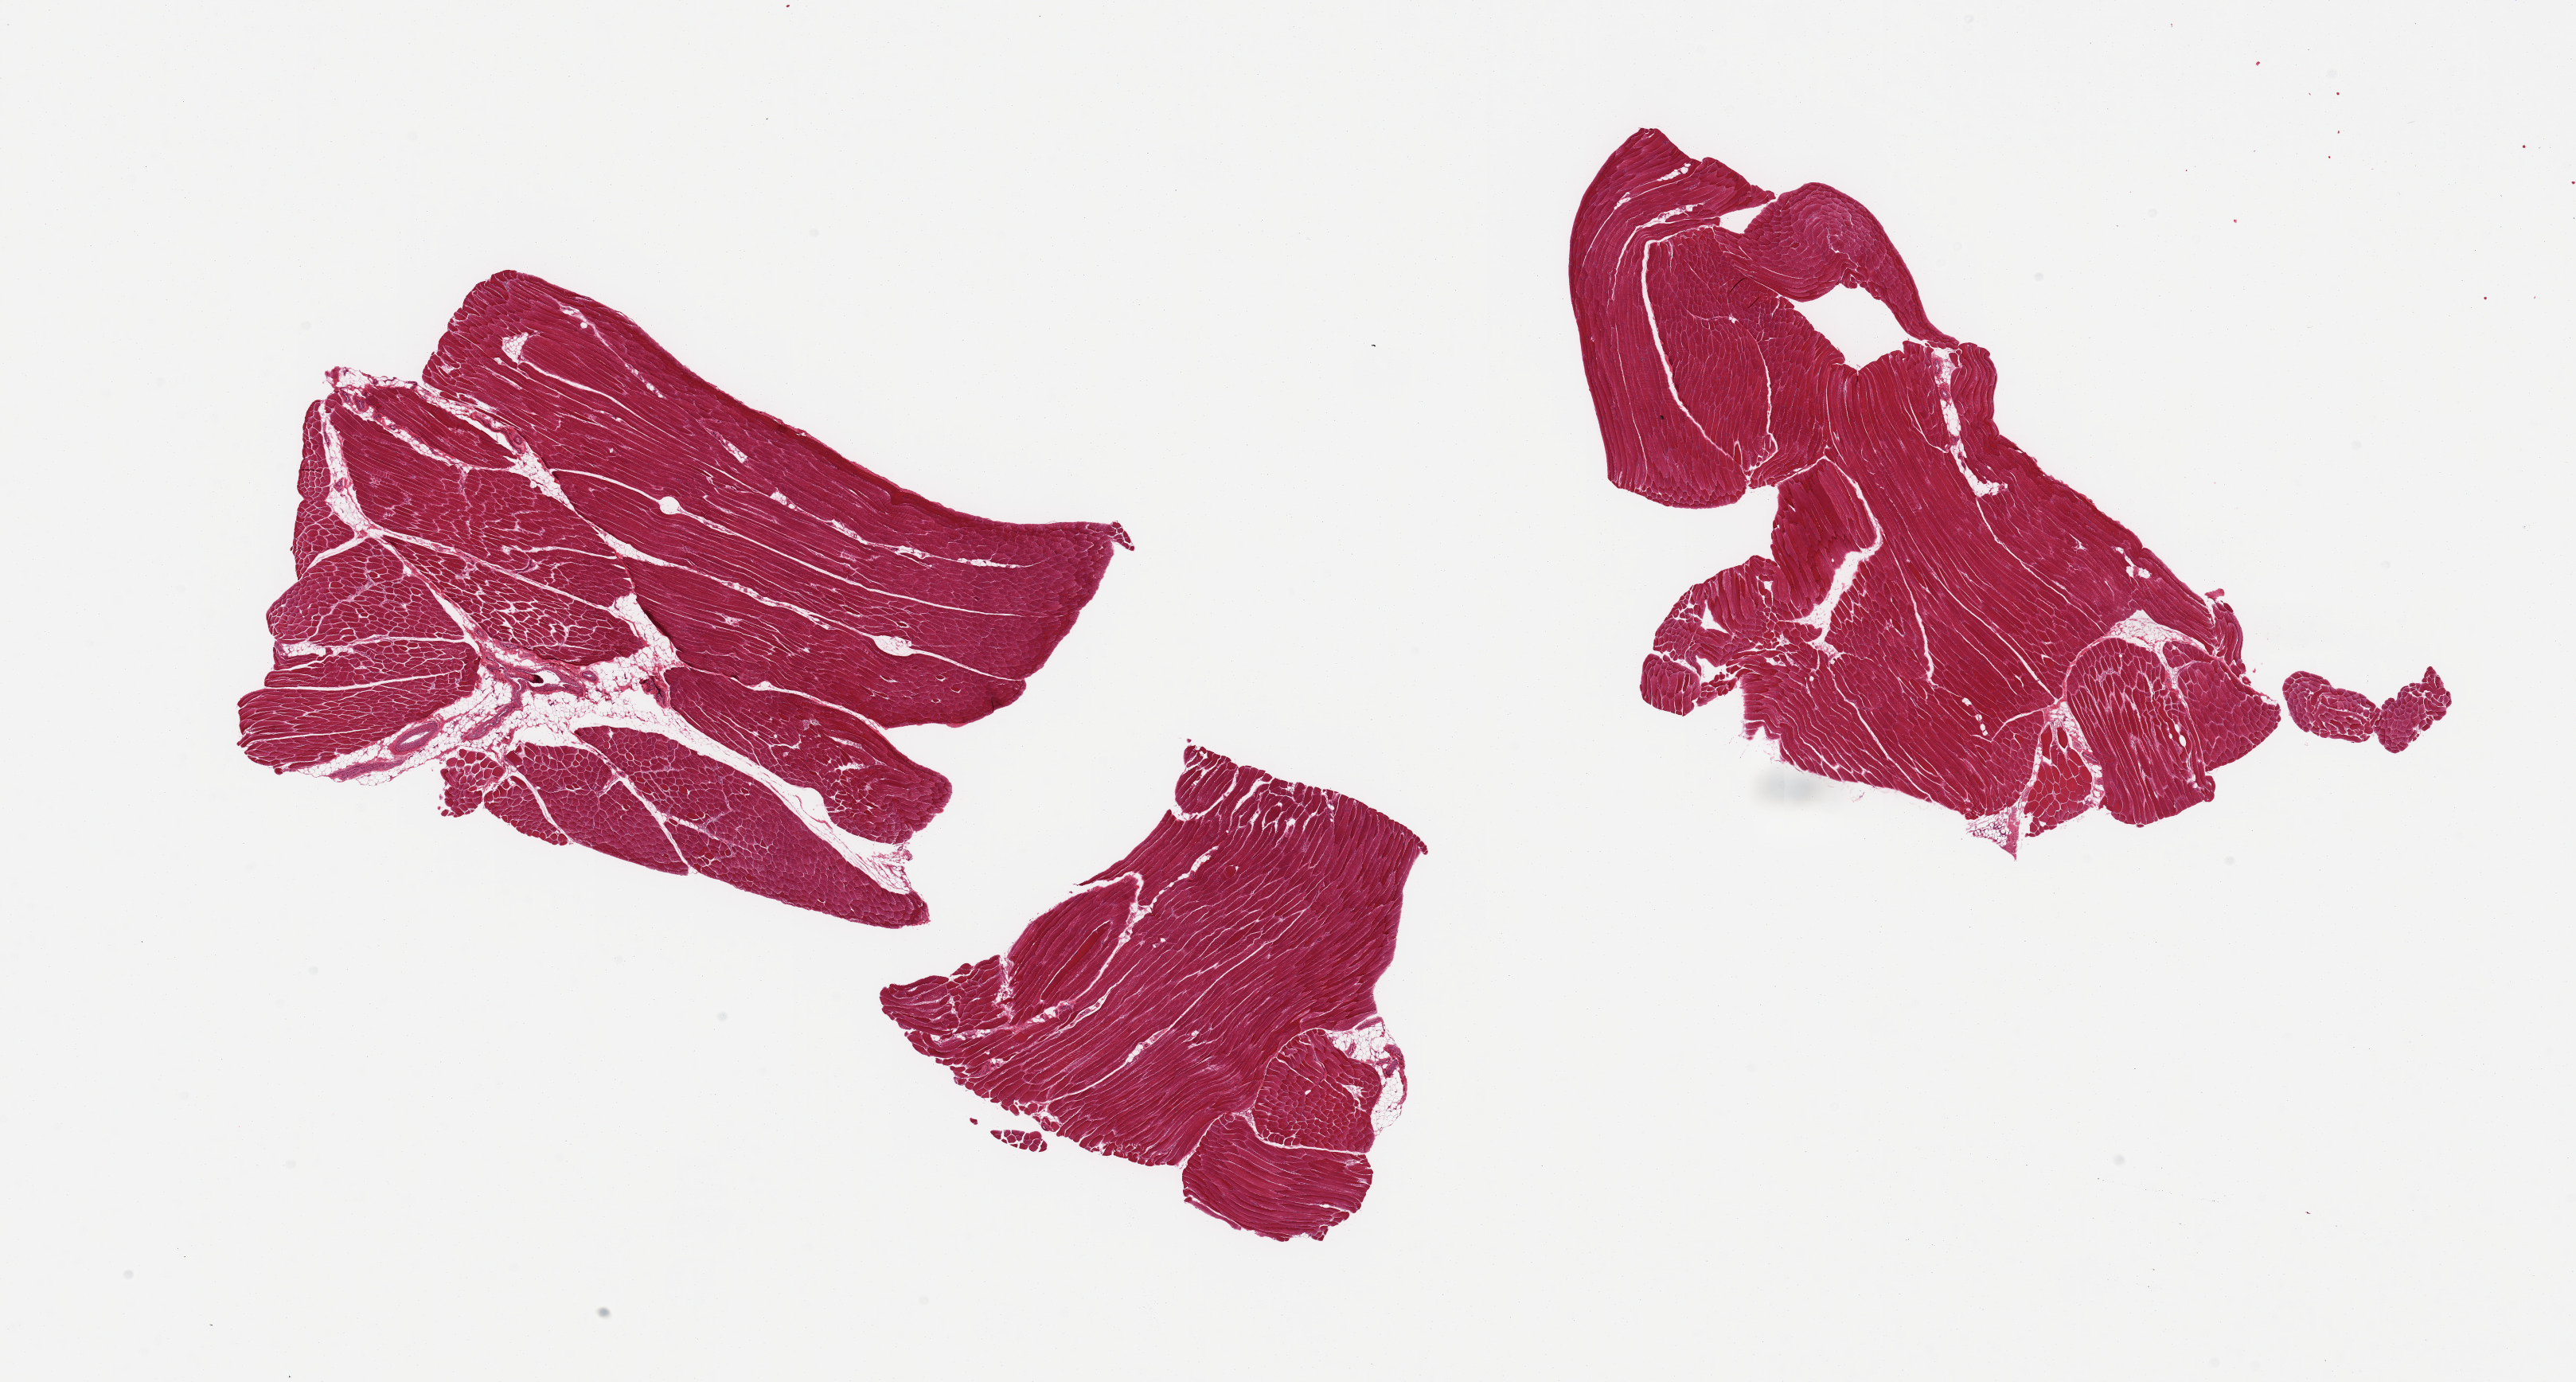
Haematoxylin and eosin whole-slide image, brightfield — shown as a low-resolution overview of the whole scanned area (about 25.6 x 13.7 mm, acquisition: 20x scan); PAXgene-fixed paraffin-embedded (PFPE) section; section of skeletal muscle (target tissue); donor tissue sample.
- reviewer comment on this tissue sample: 2 pieces; 1 piece includes ~10% internal fat, fat in 2nd is trivial